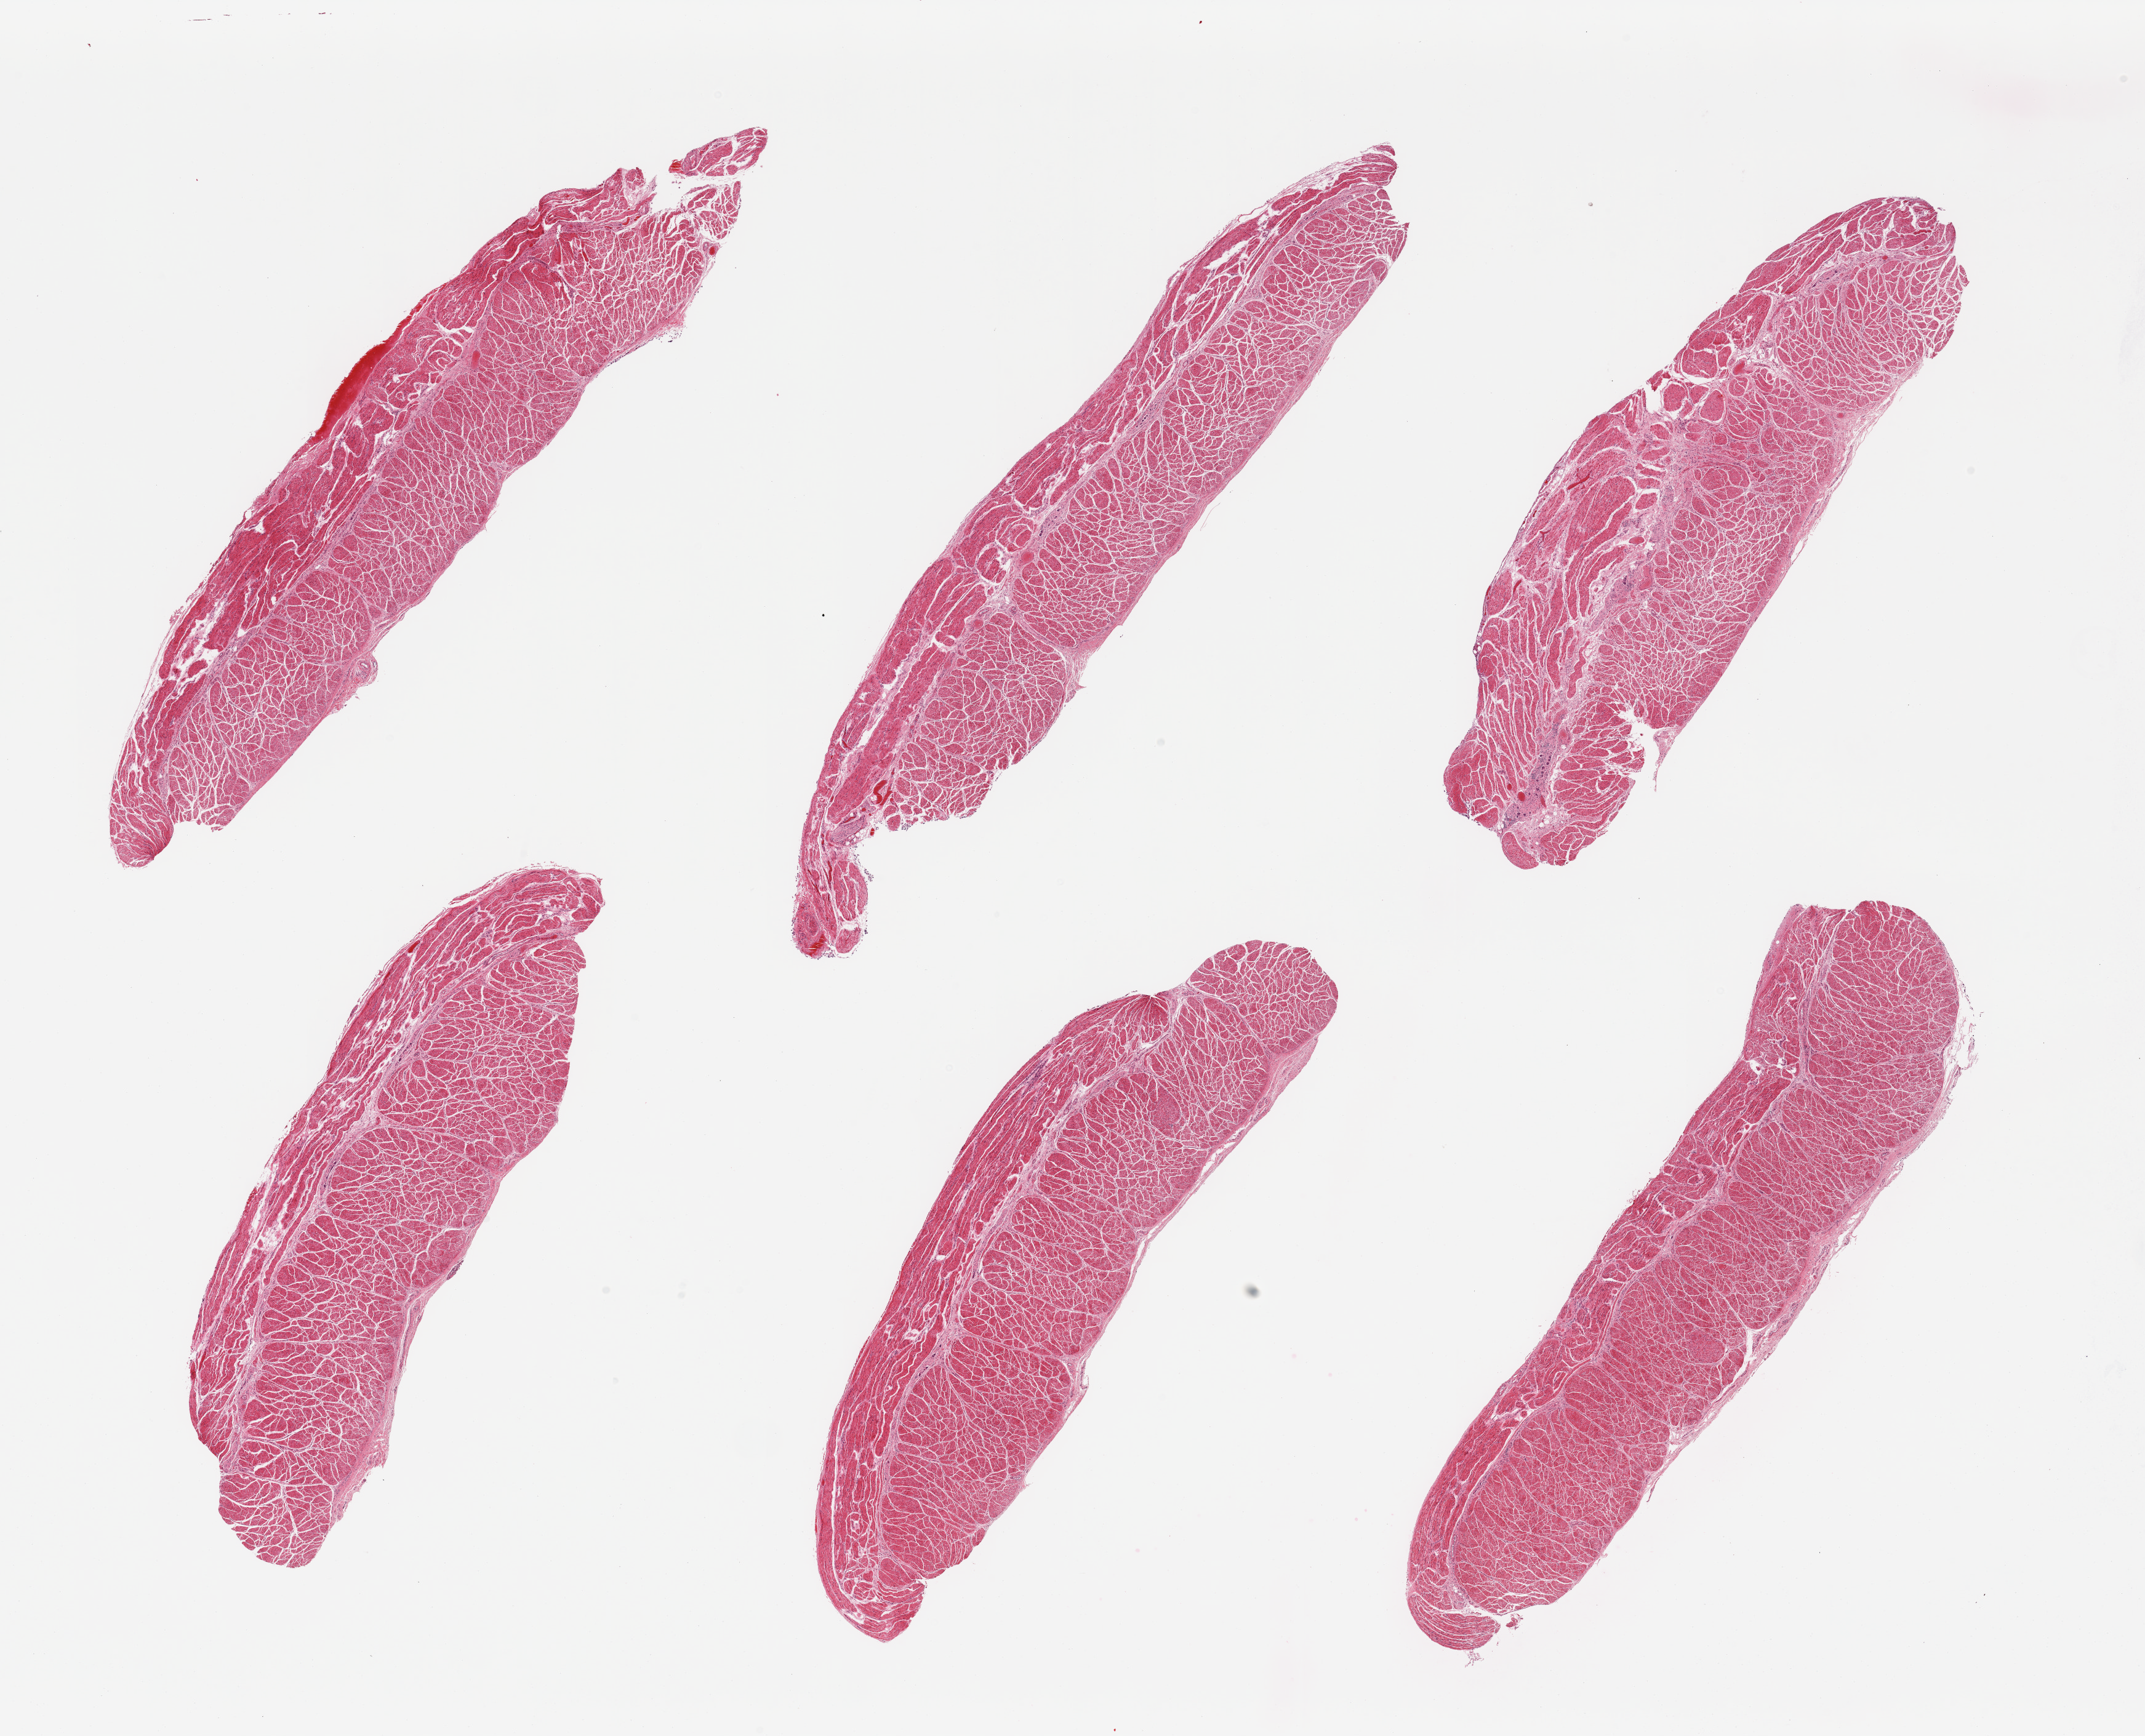
Whole-slide image, H&E stain, brightfield — whole scanned area (about 27.6 x 22.3 mm, slide scanned at 20x) shown as a low-resolution overview, PAXgene-fixed paraffin-embedded (PFPE) section, sampled site (target tissue): esophageal muscle, tissue donor sample. Donor: female.
- reviewer comment on this tissue sample: 6 pieces, all target muscularis